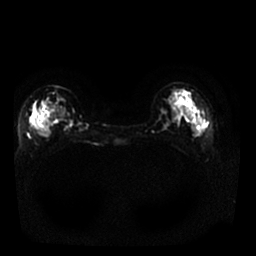
Breast MRI, one axial slice; position 8 of 25 along the scan axis; diffusion-weighted series; image 2 of 4 stored at this slice position (different b-values; order by instance number); 1.5 T; 4 mm slice thickness; 256 × 256 image matrix. Female patient.
Outlined on this slice (manually delineated by an expert):
- tumour on diffusion-weighted imaging: bounding box <32,105,37,127> (left, top, right, bottom; pixels)